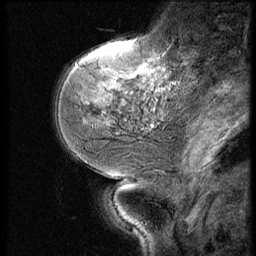
Breast MRI (dynamic contrast-enhanced), one sagittal slice; slice 18 of 56 in the series (ordered by position); dynamic contrast-enhanced series, image 2 of 3 at this slice position (ordered by acquisition); 1.5 T; TE 4.2 ms, TR 9 ms; 256 × 256 image matrix. Patient: female, 51 years. From the clinical record (not read from this slice): setting: breast cancer imaged before/during neoadjuvant chemotherapy; receptor status: triple-negative.
Structures marked on this image (semi-automatic segmentation, software-assisted and operator-edited):
- analysis volume of interest (the breast-tissue region the enhancement analysis was run in; not a lesion): bounding box <73,46,172,147> (left, top, right, bottom; pixels)
- tumour enhancement mask (voxels above the 140 % enhancement threshold inside the analysis volume of interest): <139,68,142,71>